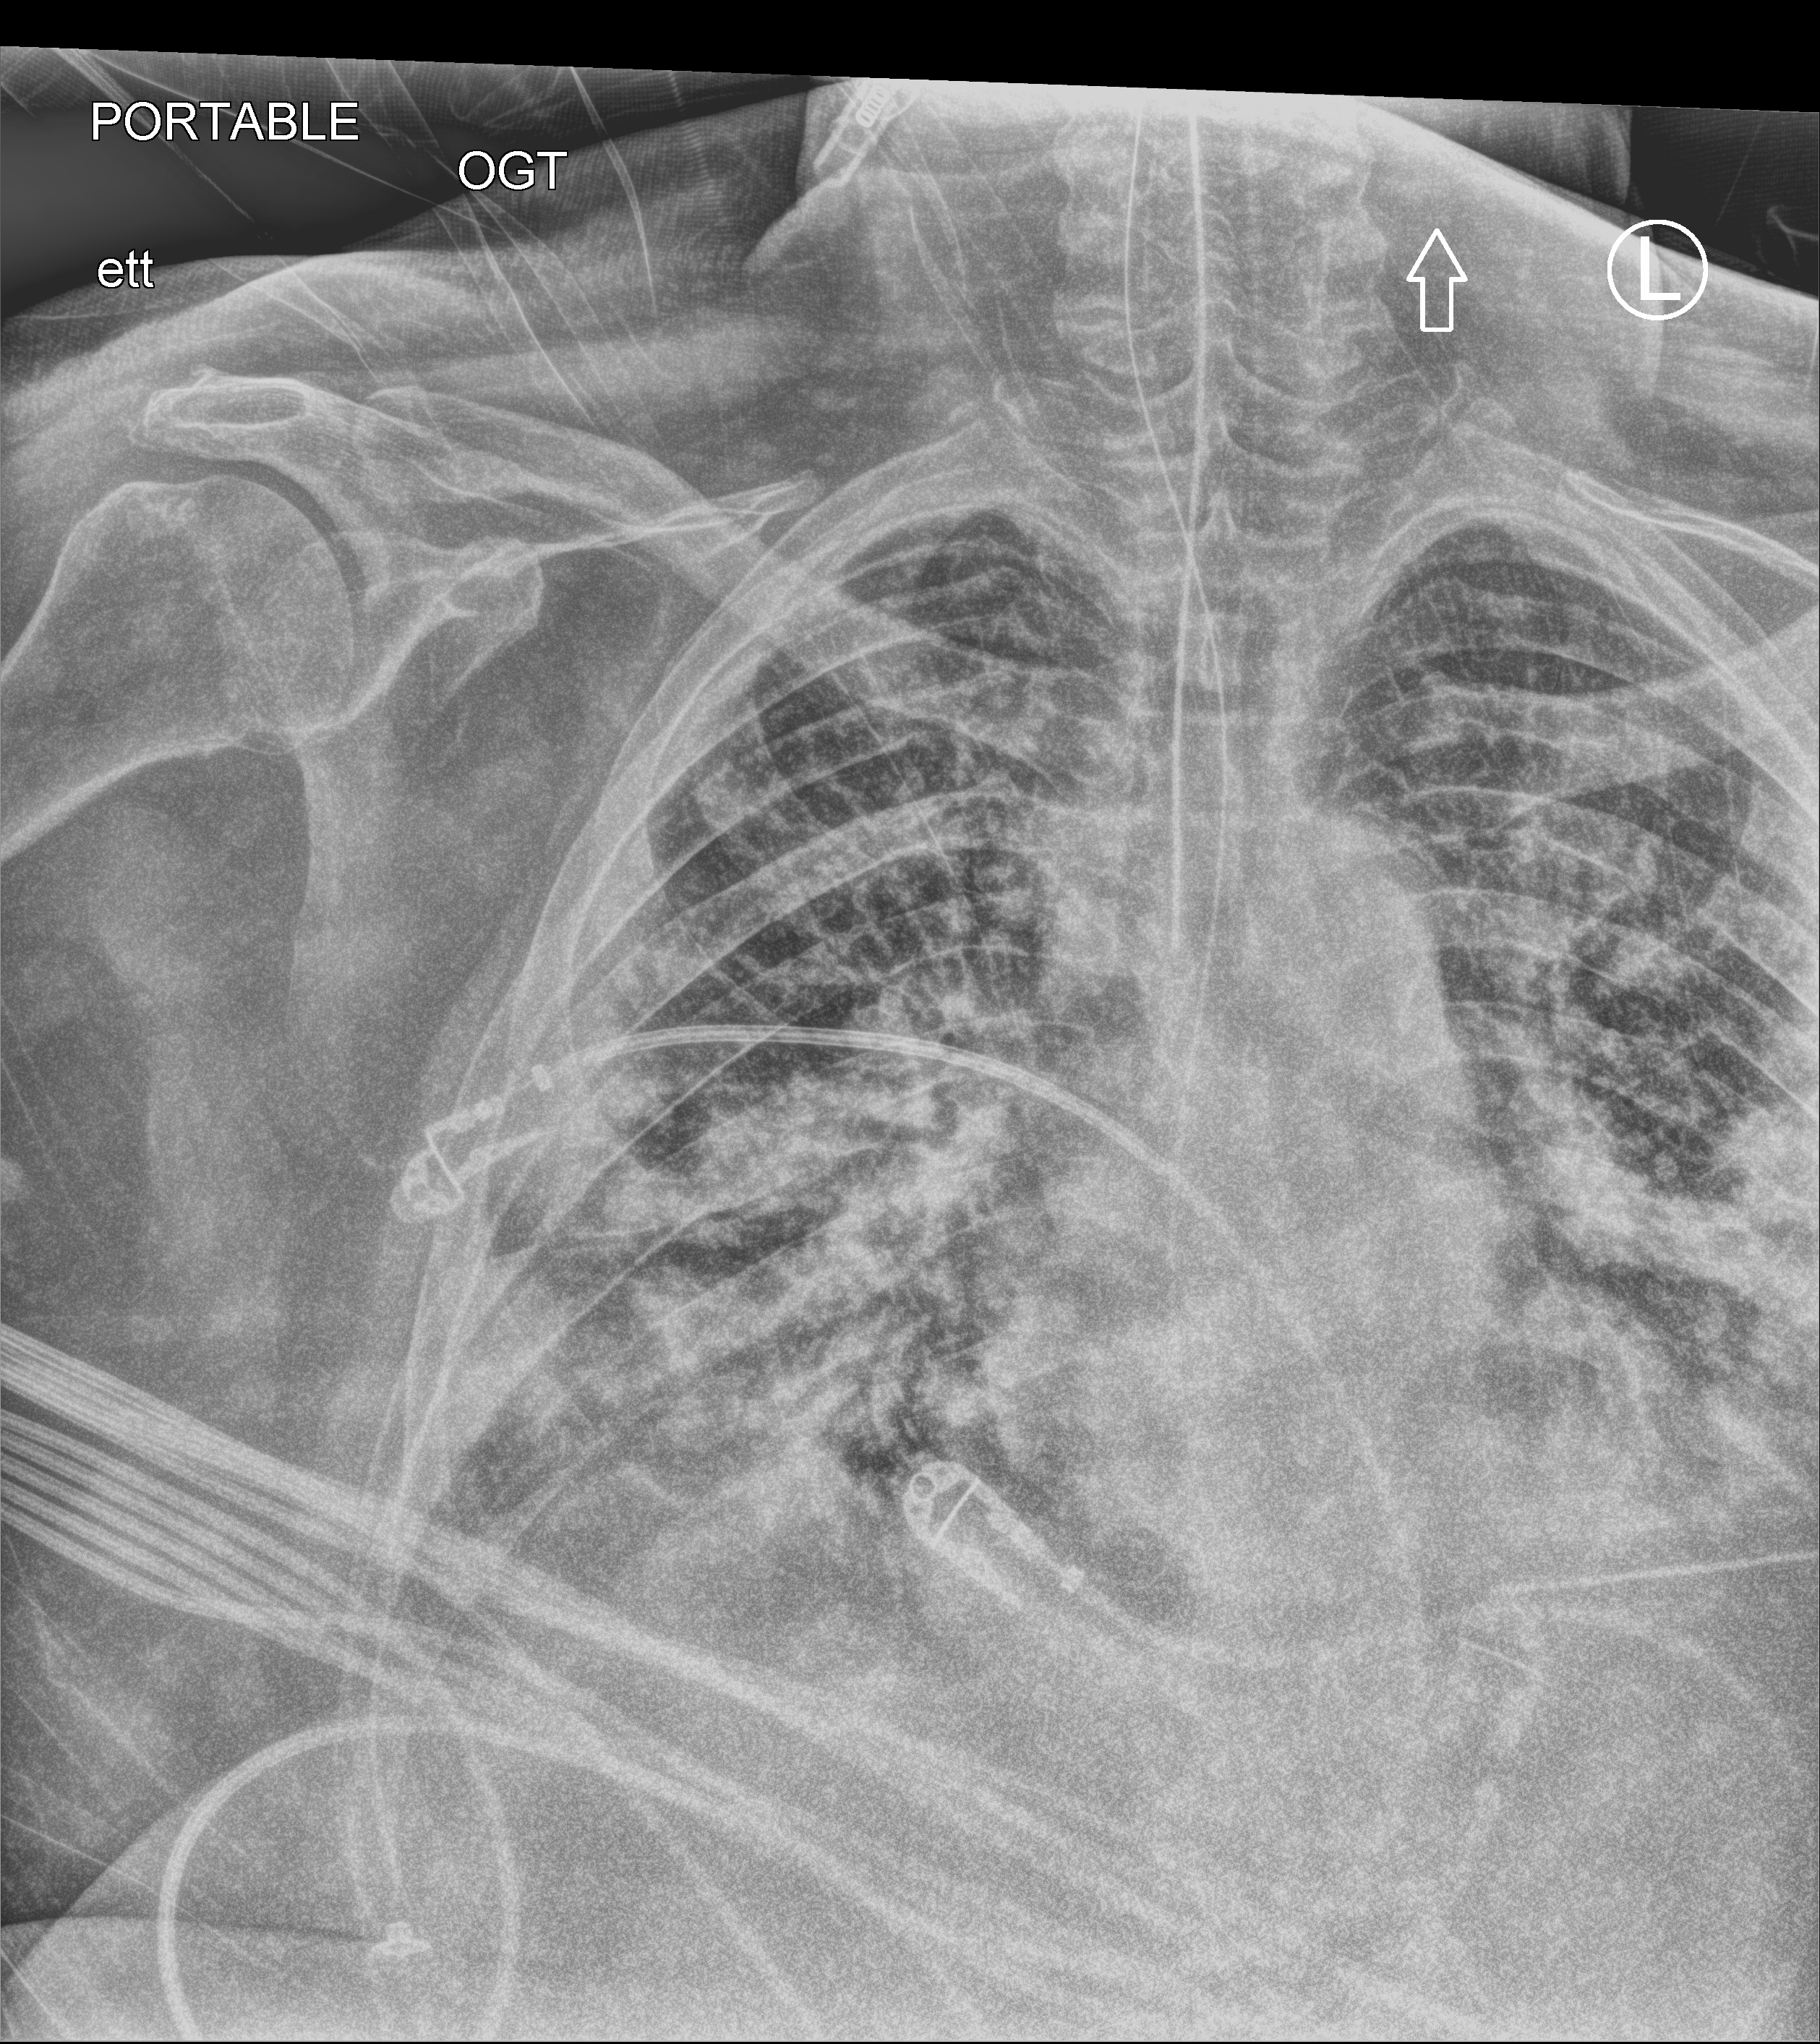
Portable chest radiograph. Patient hospitalised with COVID-19; male, aged 60–74 years.
Hospital-stay facts (about this admission, not read from this image; timing relative to this image not recorded):
- chronic kidney disease (admission record): yes
- other chronic lung disease (admission record): no
- mechanically ventilated during this hospital stay: yes